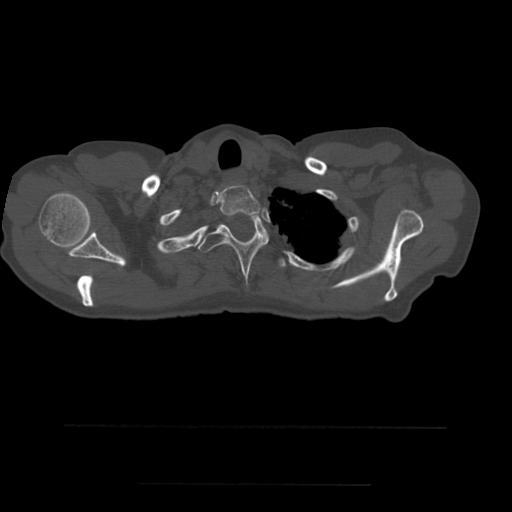
CT including the spine, one axial slice; position 437 of 544 along the scan axis; bone window (W 1800 / L 400 HU); 1.25 mm slice thickness; 512 × 512 image matrix, field of view 350 × 350 mm. Patient age 58 years. From the clinical record (not read from this slice): primary cancer: lung.
Annotated regions visible in this slice (semi-automatically segmented with operator editing):
- T1 vertebra: box from (x=220, y=184) to (x=261, y=217) px
- T2 vertebra: (x=198, y=214)–(x=269, y=281)
- T3 vertebra: (x=279, y=259)–(x=286, y=268)